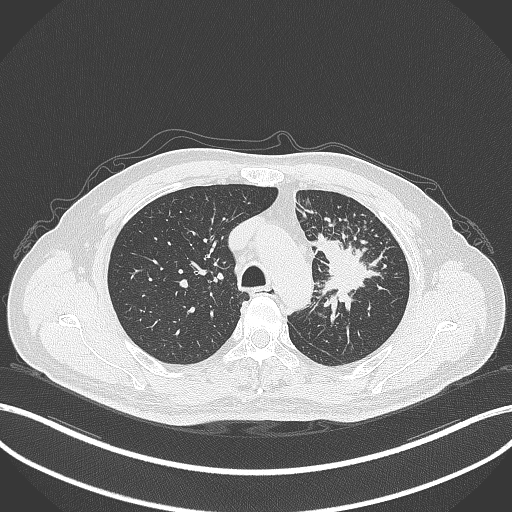
Chest CT, one axial slice. Position 264 of 386 along the scan axis. Reconstruction kernel B70f. 120 kVp. Lung window (W 1500 / L -600 HU). 1 mm slice thickness. 512 × 512 image matrix, field of view 400 × 400 mm. Patient: male, 69 years. Case-level facts recorded for this patient, not image findings: clinical TNM (as recorded): T2a N2 M0; histopathological grade: G2-3.
Outlined on this slice (bounding box drawn by a radiologist):
- lung tumour (recorded histology: adenocarcinoma): bounding box [x1, y1, x2, y2] px = [310, 227, 384, 313]